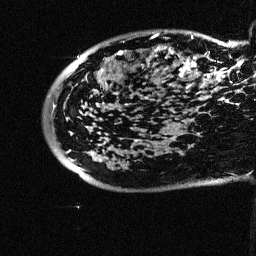
Breast MRI (dynamic contrast-enhanced), one sagittal slice. Slice 13 of 64 in the series (ordered by position). Dynamic contrast-enhanced study with each time point stored as its own series, time point 2 of 3 at this slice position (early post-contrast, ordered by acquisition time). 1.5 T. TE 4.5 ms, TR 11 ms. 2.5 mm slice thickness. 256 × 256 image matrix, field of view 200 × 200 mm. Patient: female, 38 years. Case-level facts recorded for this patient, not image findings: setting: breast cancer imaged before/during neoadjuvant chemotherapy; receptor status: HR-positive, HER2-negative.
Outlined on this slice (semi-automatic segmentation, software-assisted and operator-edited):
- analysis volume of interest (the breast-tissue region the enhancement analysis was run in; not a lesion): box from (x=88, y=23) to (x=252, y=126) px
- tumour enhancement mask (voxels above the 90 % enhancement threshold inside the analysis volume of interest): (x=117, y=34)–(x=246, y=83)